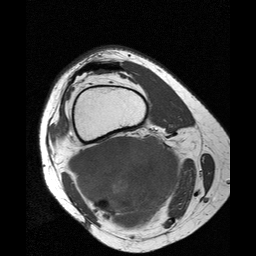
MRI of an extremity soft-tissue mass, one axial slice. Position 19 of 25 along the scan axis. 256 × 256 image matrix, field of view 160 × 160 mm. Female patient. From the clinical record (not read from this slice): histological type: liposarcoma; site of the primary tumour: right thigh.
Annotated regions visible in this slice (manually delineated by an expert):
- gross tumour volume (mass): bounding box [x1, y1, x2, y2] px = [68, 135, 184, 231]